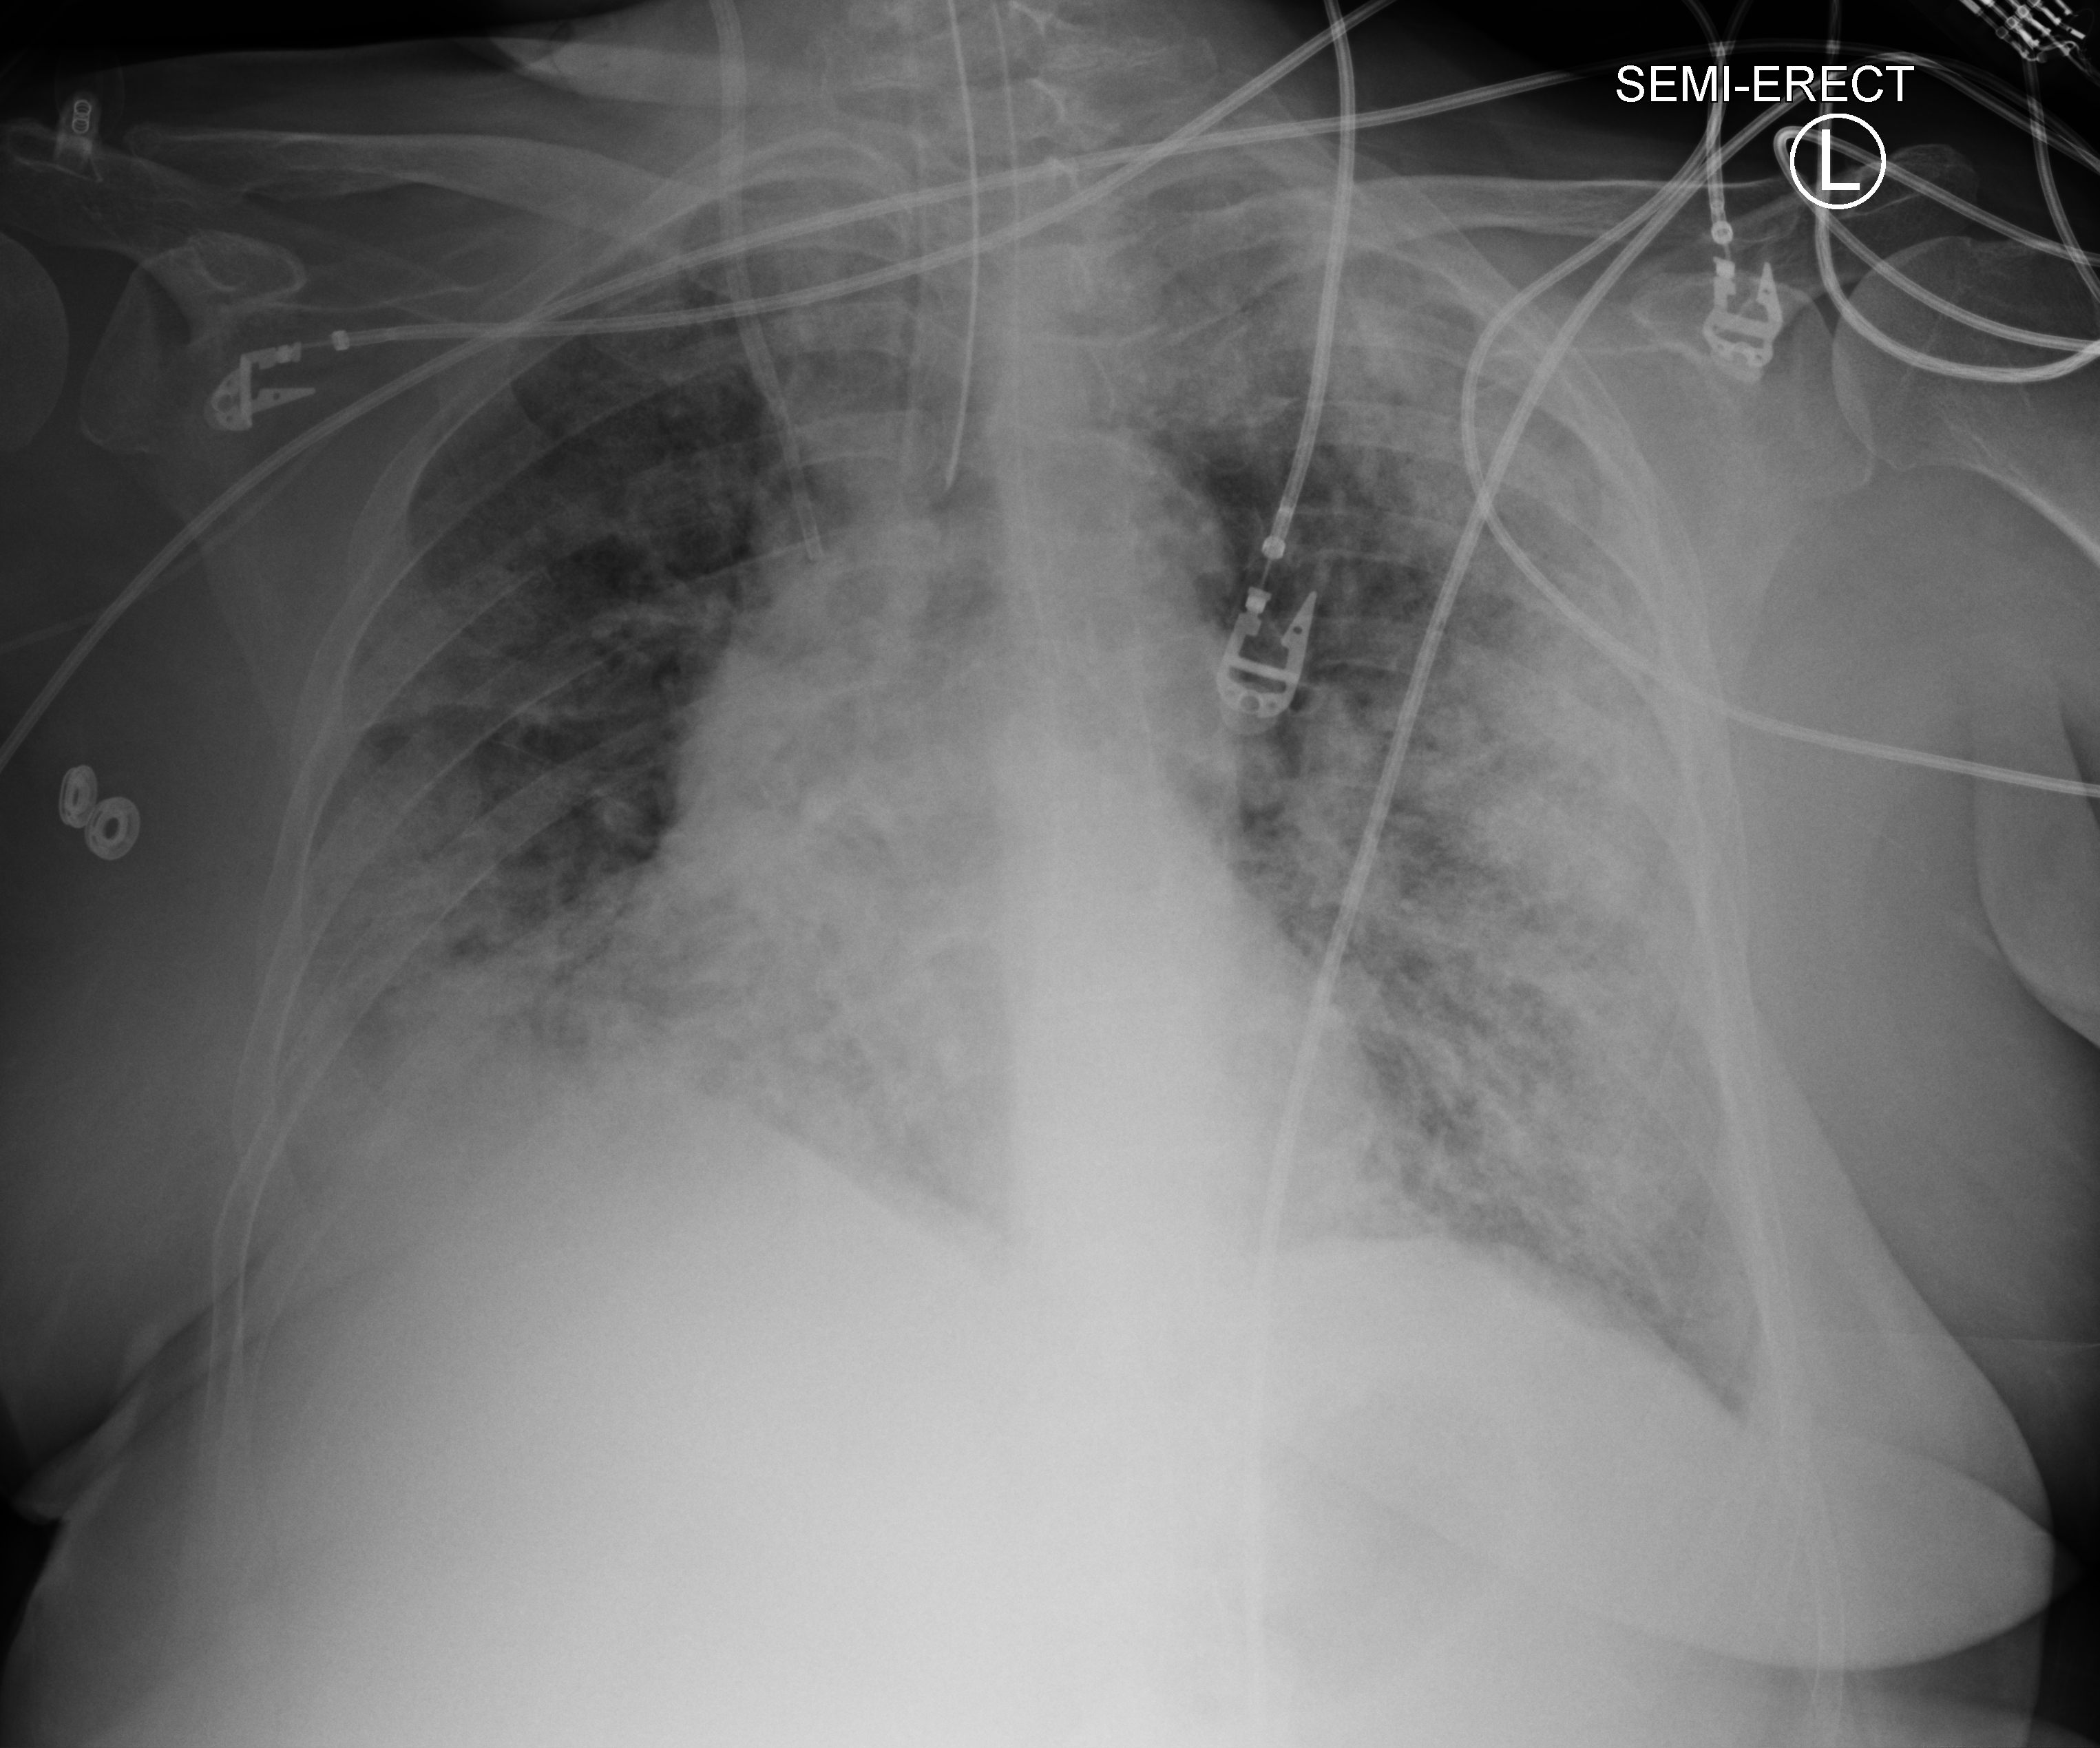
Chest X-ray (portable); anteroposterior (AP) projection. Patient hospitalised with COVID-19; female, aged 75–90 years.
From the hospital-stay record, not from the radiograph (when in the stay this image was taken is not recorded): diabetes (admission record): no; length of hospital stay: 28 days.